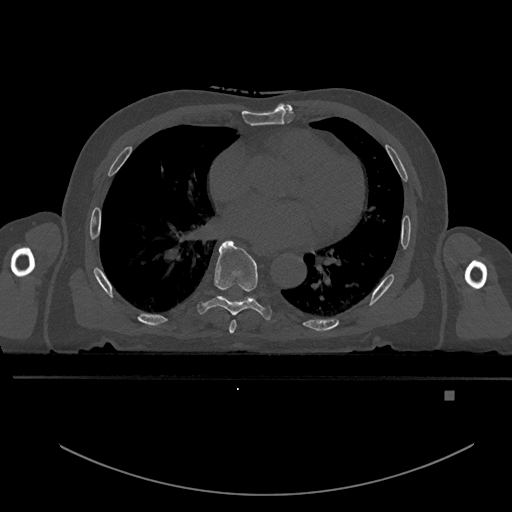
CT including the spine, one axial slice. Bone window (W 1800 / L 400 HU). 512 × 512 image matrix. Patient: male, 82 years. From the clinical record (not read from this slice): primary cancer: prostate; vertebrae with lytic lesions (as recorded): T11, T9, T8, T2.
Structures marked on this image (semi-automatically segmented with operator editing):
- T6 vertebra: box from (x=229, y=320) to (x=236, y=334) px
- T7 vertebra: (x=197, y=240)–(x=272, y=320)
- T8 vertebra: (x=221, y=295)–(x=256, y=302)